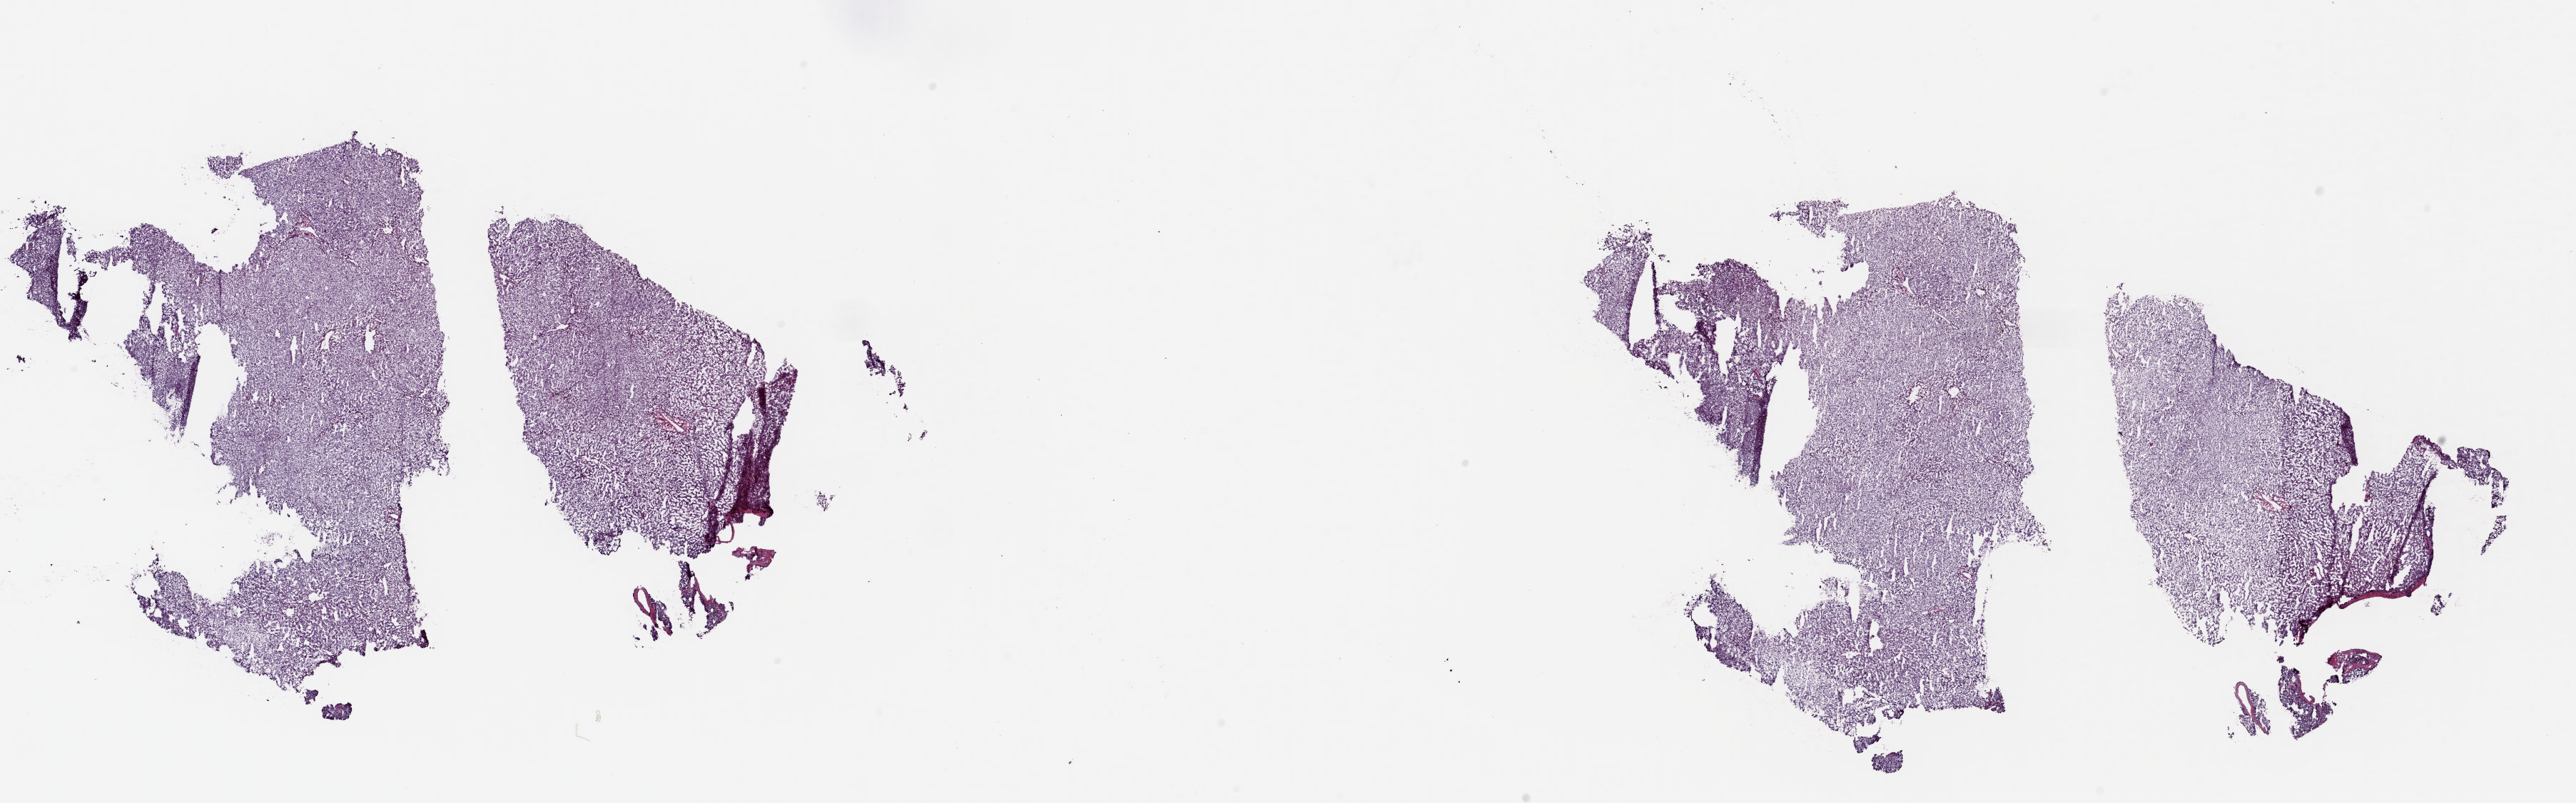
Digitized H&E-stained tissue section (whole slide) — low-resolution overview of the scanned area, about 28.7 x 8.9 mm (from a 20x scan), frozen section from the top of the tissue portion, sample: solid tissue normal (non-tumour tissue), liver. Female patient; age at initial diagnosis 72 years. Composition of this section per pathologist review: tumour cells 0%, tumour nuclei 0%, normal cells 100%, stromal cells 0%, necrosis 0%. Infiltration values recorded for this section: lymphocyte infiltration 0%, monocyte infiltration 0%, neutrophil infiltration 0%.
This section: solid tissue normal sample (biorepository sample class). Patient diagnosis: Hepatocellular carcinoma, NOS.